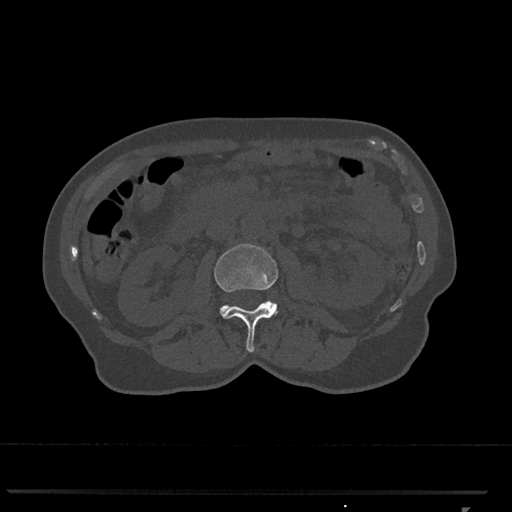
CT including the spine, one axial slice. Position 328 of 793 along the scan axis. Reconstruction kernel Br40s/3. Bone window (W 1800 / L 400 HU). 0.5 mm slice thickness. 512 × 512 image matrix, field of view 380 × 380 mm. Patient: female, 62 years. Case-level facts recorded for this patient, not image findings: primary cancer: renal.
Structures marked on this image (semi-automatically segmented with operator editing):
- L2 vertebra: bounding box <214,243,279,352> (left, top, right, bottom; pixels)